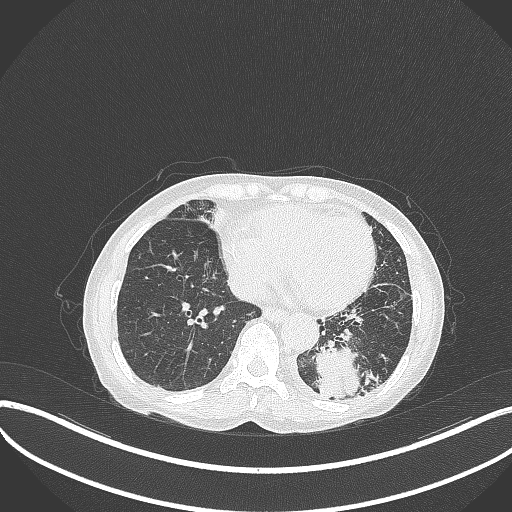
Chest CT, one axial slice; slice 93 of 370 in the series (ordered by position); reconstruction kernel B70f; 120 kVp; lung window (W 1500 / L -600 HU); 512 × 512 image matrix. Female patient, age 78 years. From the clinical record (not read from this slice): clinical TNM (as recorded): T3 N0 M1.
Annotated regions visible in this slice (rectangle marked by the reading radiologist):
- lung tumour (recorded histology: squamous cell carcinoma): bounding box (x1, y1, x2, y2) in pixels: (311, 339, 365, 400)